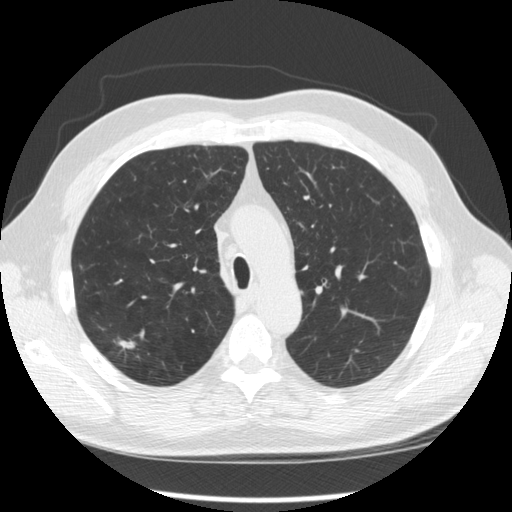
Low-dose screening chest CT, axial slice. Second annual screen. Lung window (W 1500 / L -600 HU). Slice 81 of 289 in the series. 512 × 512 image matrix. Male, age 64 years at enrolment. Former smoker at enrolment.
Expert-annotated lung lesion, bounding box <104,326,149,367> (left, top, right, bottom; pixels). The screening reader recorded 3 non-calcified nodules or masses ≥4 mm on this exam (right upper lobe, right upper lobe, right upper lobe); which of them this box marks is not recorded. Official screen result: positive, other.